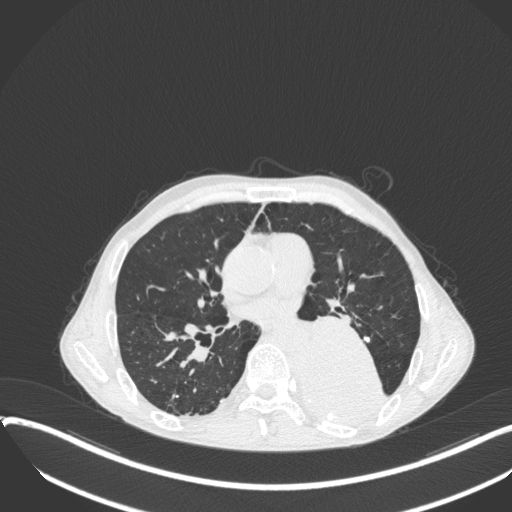
Chest CT, one axial slice; position 189 of 400 along the scan axis; reconstruction kernel B31f; lung window (W 1500 / L -600 HU); 1 mm slice thickness; 512 × 512 image matrix, field of view 400 × 400 mm. Patient: male, 57 years. From the clinical record (not read from this slice): clinical TNM (as recorded): T4 N0 M0.
Outlined on this slice (rectangle marked by the reading radiologist):
- lung tumour (recorded histology: squamous cell carcinoma): bounding box <294,307,385,421> (left, top, right, bottom; pixels)